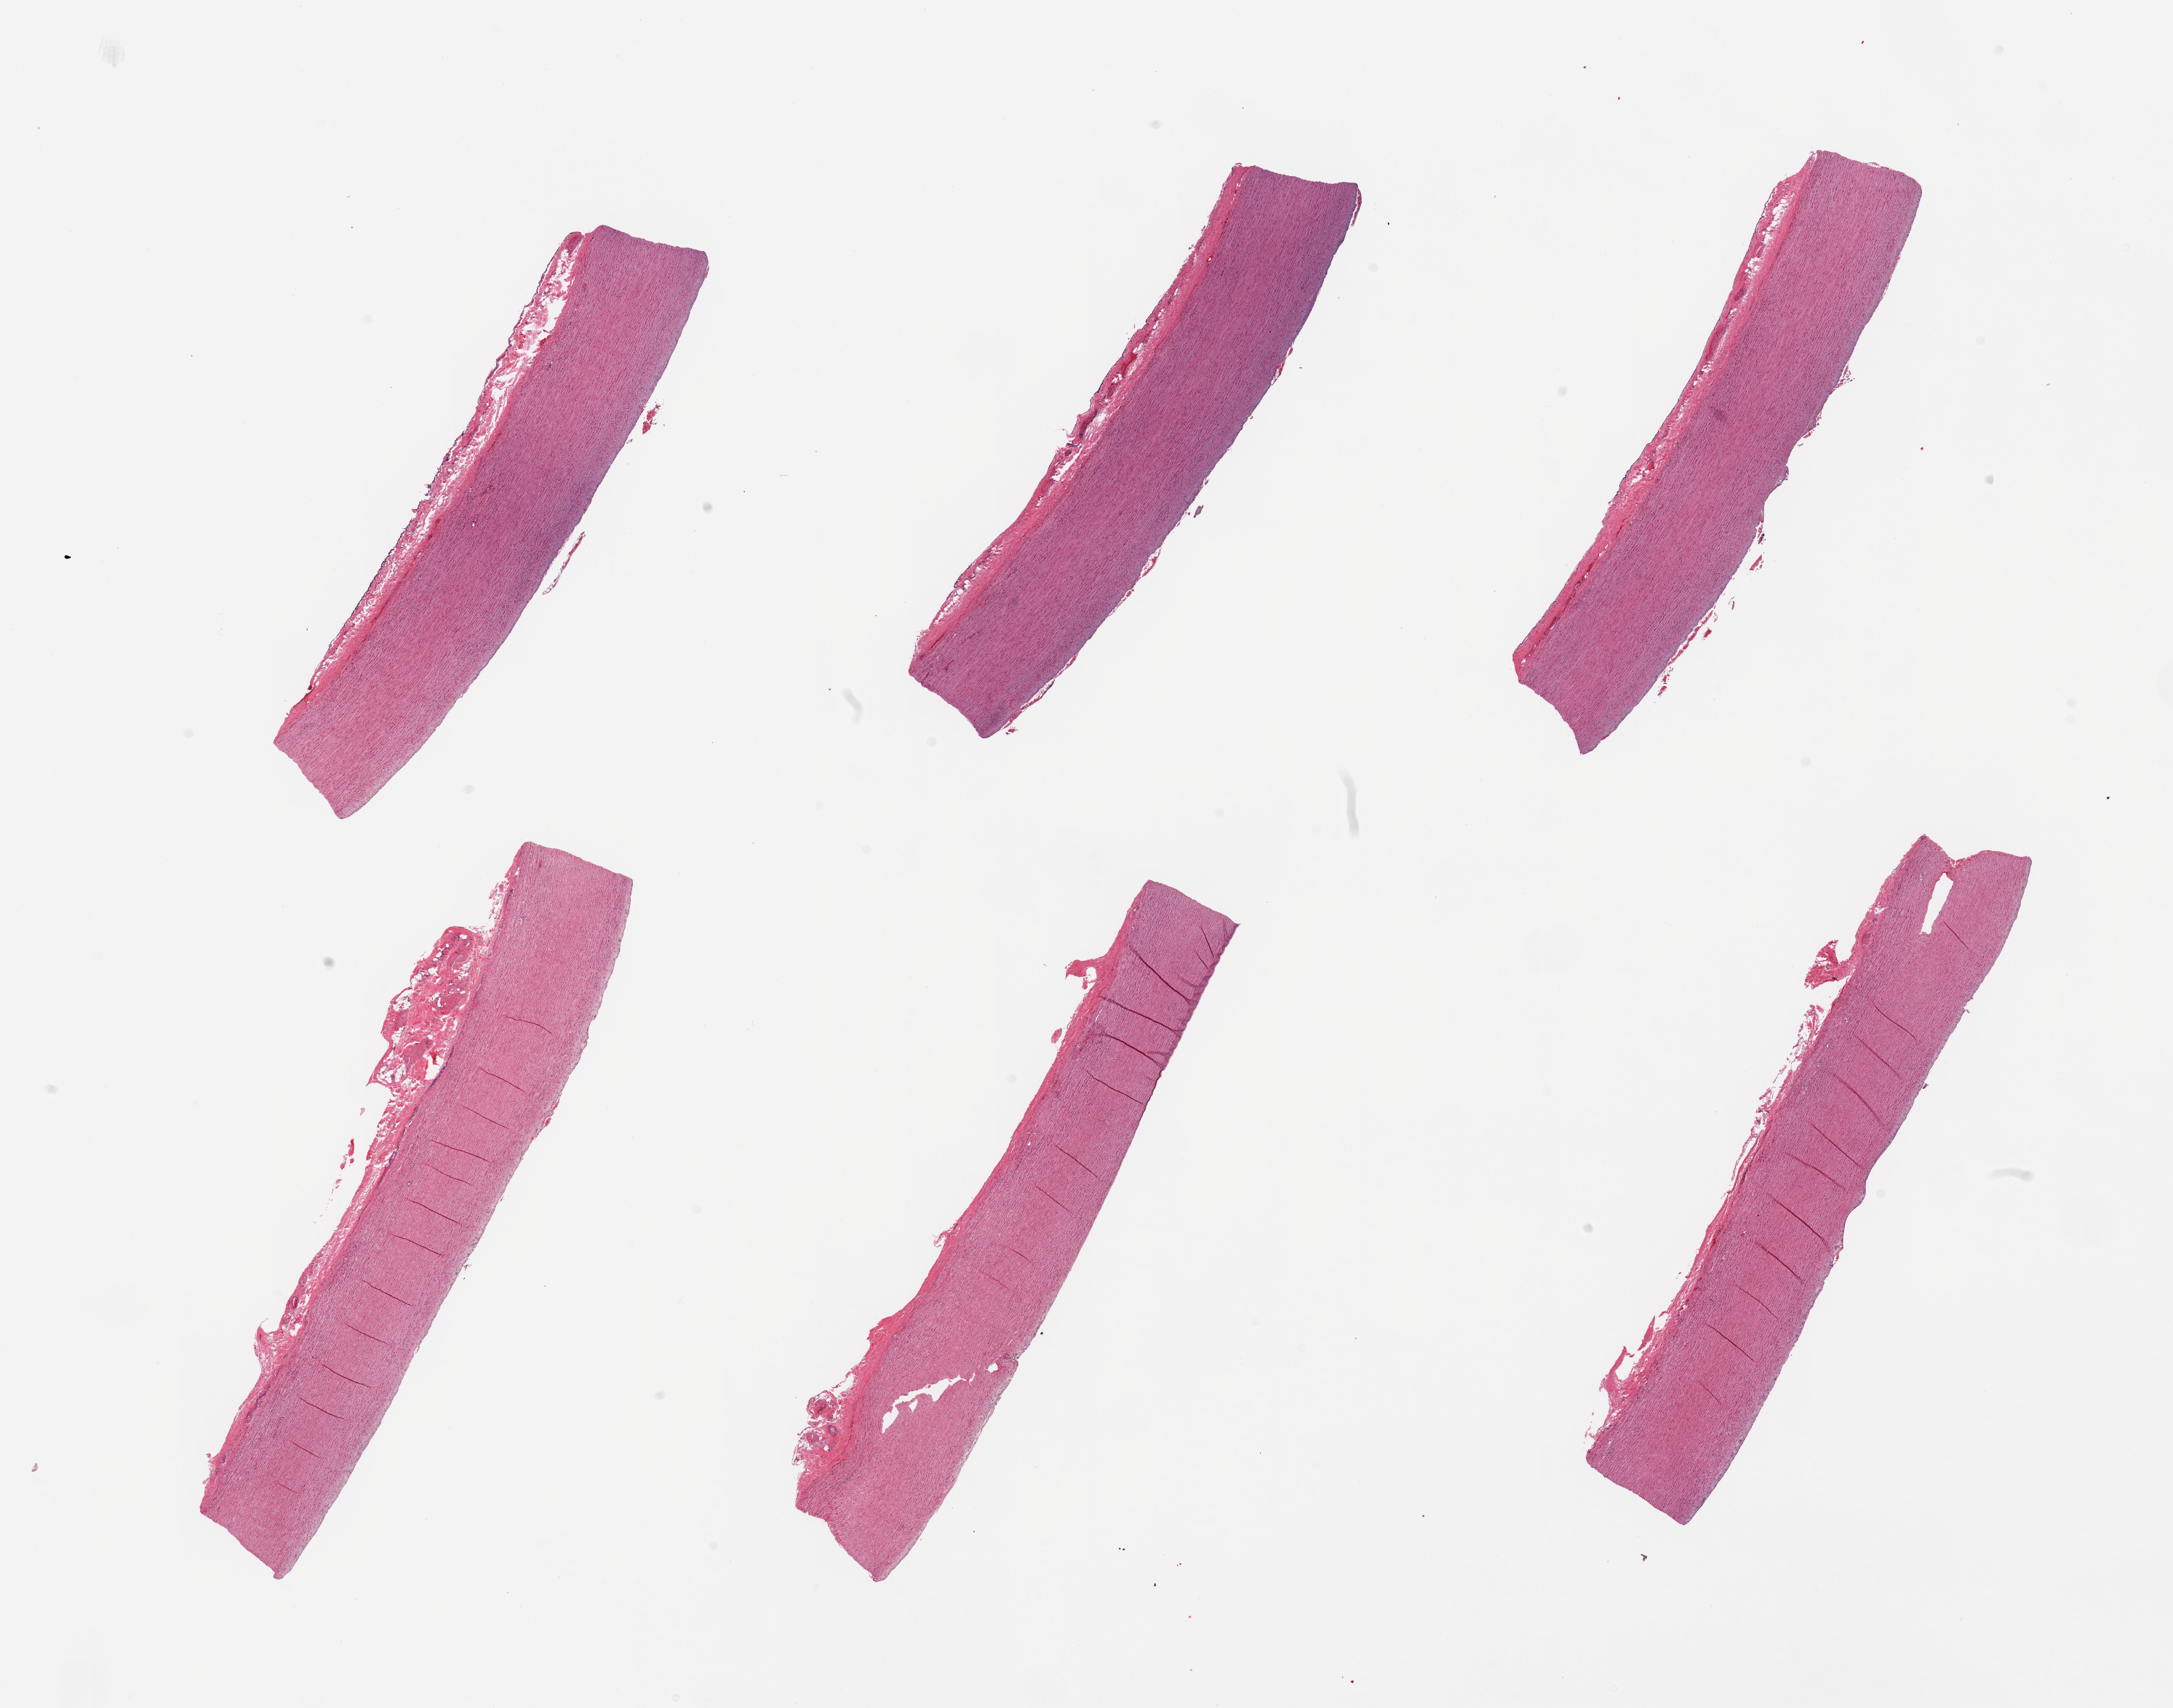
H&E whole-slide image — low-resolution overview of the scanned area, about 23.6 x 18.6 mm (from a 20x scan); PAXgene-fixed paraffin-embedded (PFPE) section; section of aorta (target tissue); donor tissue sample. Female donor.
- reviewer comment on this tissue sample: 6 pieces; no lesions; well trimmed